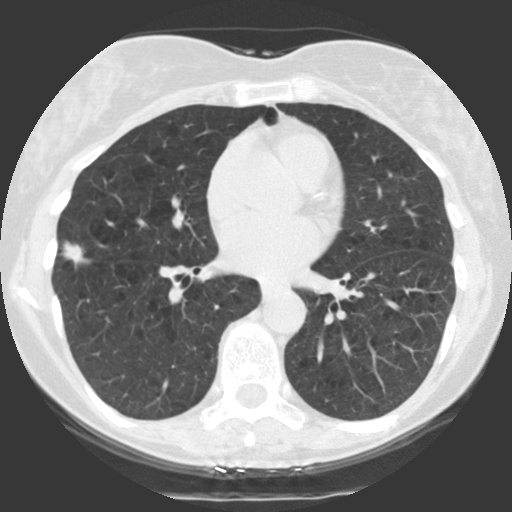
Low-dose screening chest CT, one axial slice; slice 57 of 123 in the series (ordered by position); 140 kVp; lung window (W 1500 / L -600 HU); 512 × 512 image matrix, field of view 290 × 290 mm.
Annotated regions visible in this slice (outlined manually by an expert reader):
- lesion 1 (tumor, middle lobe of right lung): bounding box [x1, y1, x2, y2] px = [62, 242, 88, 266]